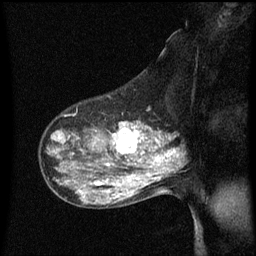
Breast MRI (dynamic contrast-enhanced), one sagittal slice; position 41 of 60 along the scan axis; dynamic contrast-enhanced series, image 2 of 3 at this slice position (ordered by acquisition); 1.5 T; TE 4.2 ms, TR 8.4 ms; 2 mm slice thickness; 256 × 256 image matrix, field of view 200 × 200 mm. Female patient, age 50 years.
Structures marked on this image (semi-automatically segmented with operator editing):
- analysis volume of interest (the breast-tissue region the enhancement analysis was run in; not a lesion): bounding box [x1, y1, x2, y2] px = [100, 118, 153, 171]
- tumour enhancement mask (voxels above the 70 % enhancement threshold inside the analysis volume of interest): [106, 122, 150, 167]